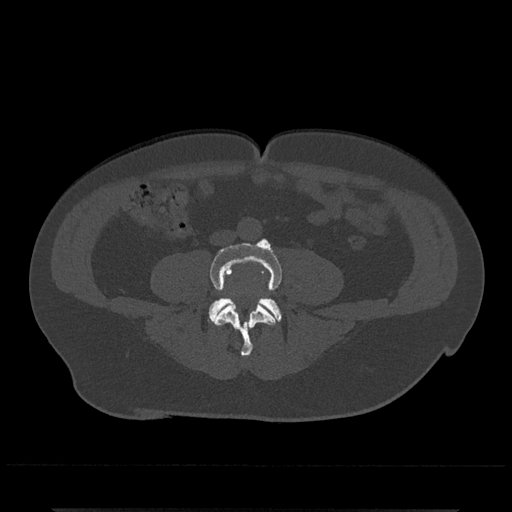
CT including the spine, one axial slice; position 130 of 797 along the scan axis; reconstruction kernel Br40s/3; 120 kVp; bone window (W 1800 / L 400 HU); 0.5 mm slice thickness; 512 × 512 image matrix, field of view 393 × 393 mm. Patient: male, 67 years. Case-level facts recorded for this patient, not image findings: primary cancer: prostate.
Structures marked on this image (semi-automatically segmented with operator editing):
- L4 vertebra: bounding box [x1, y1, x2, y2] px = [210, 239, 282, 357]
- L5 vertebra: [208, 297, 282, 322]